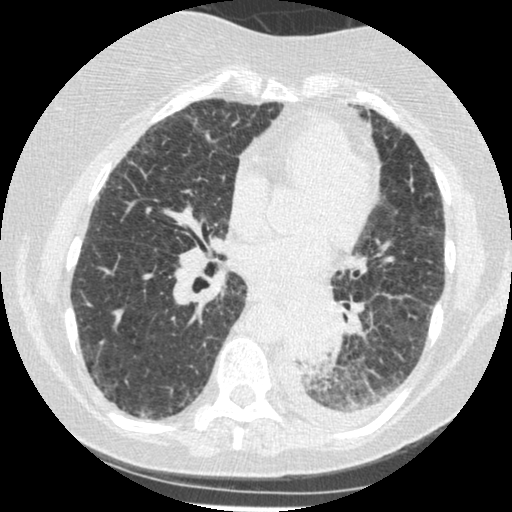
Low-dose screening chest CT, one axial slice. Position 107 of 341 along the scan axis. Reconstruction kernel STANDARD. 120 kVp. Lung window (W 1500 / L -600 HU). 512 × 512 image matrix, field of view 310 × 310 mm.
Structures marked on this image (outlined manually by an expert reader):
- lesion 1 (tumor, lower lobe of left lung): box from (x=285, y=303) to (x=338, y=364) px